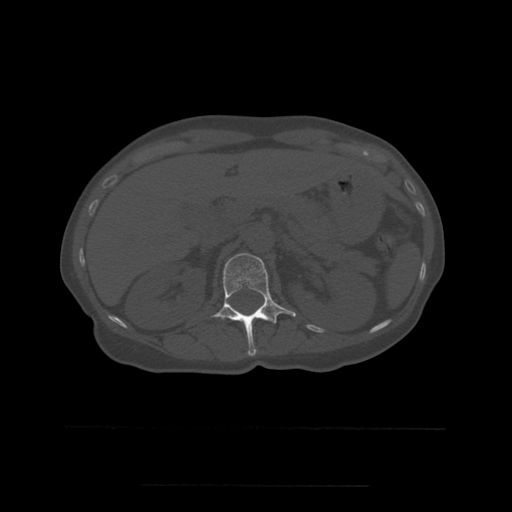
CT including the spine, one axial slice; bone window (W 1800 / L 400 HU); 1.25 mm slice thickness; 512 × 512 image matrix, field of view 350 × 350 mm. Patient age 58 years. Case-level facts recorded for this patient, not image findings: primary cancer: lung.
Outlined on this slice (semi-automatic segmentation, software-assisted and operator-edited):
- L1 vertebra: bounding box <212,253,296,356> (left, top, right, bottom; pixels)